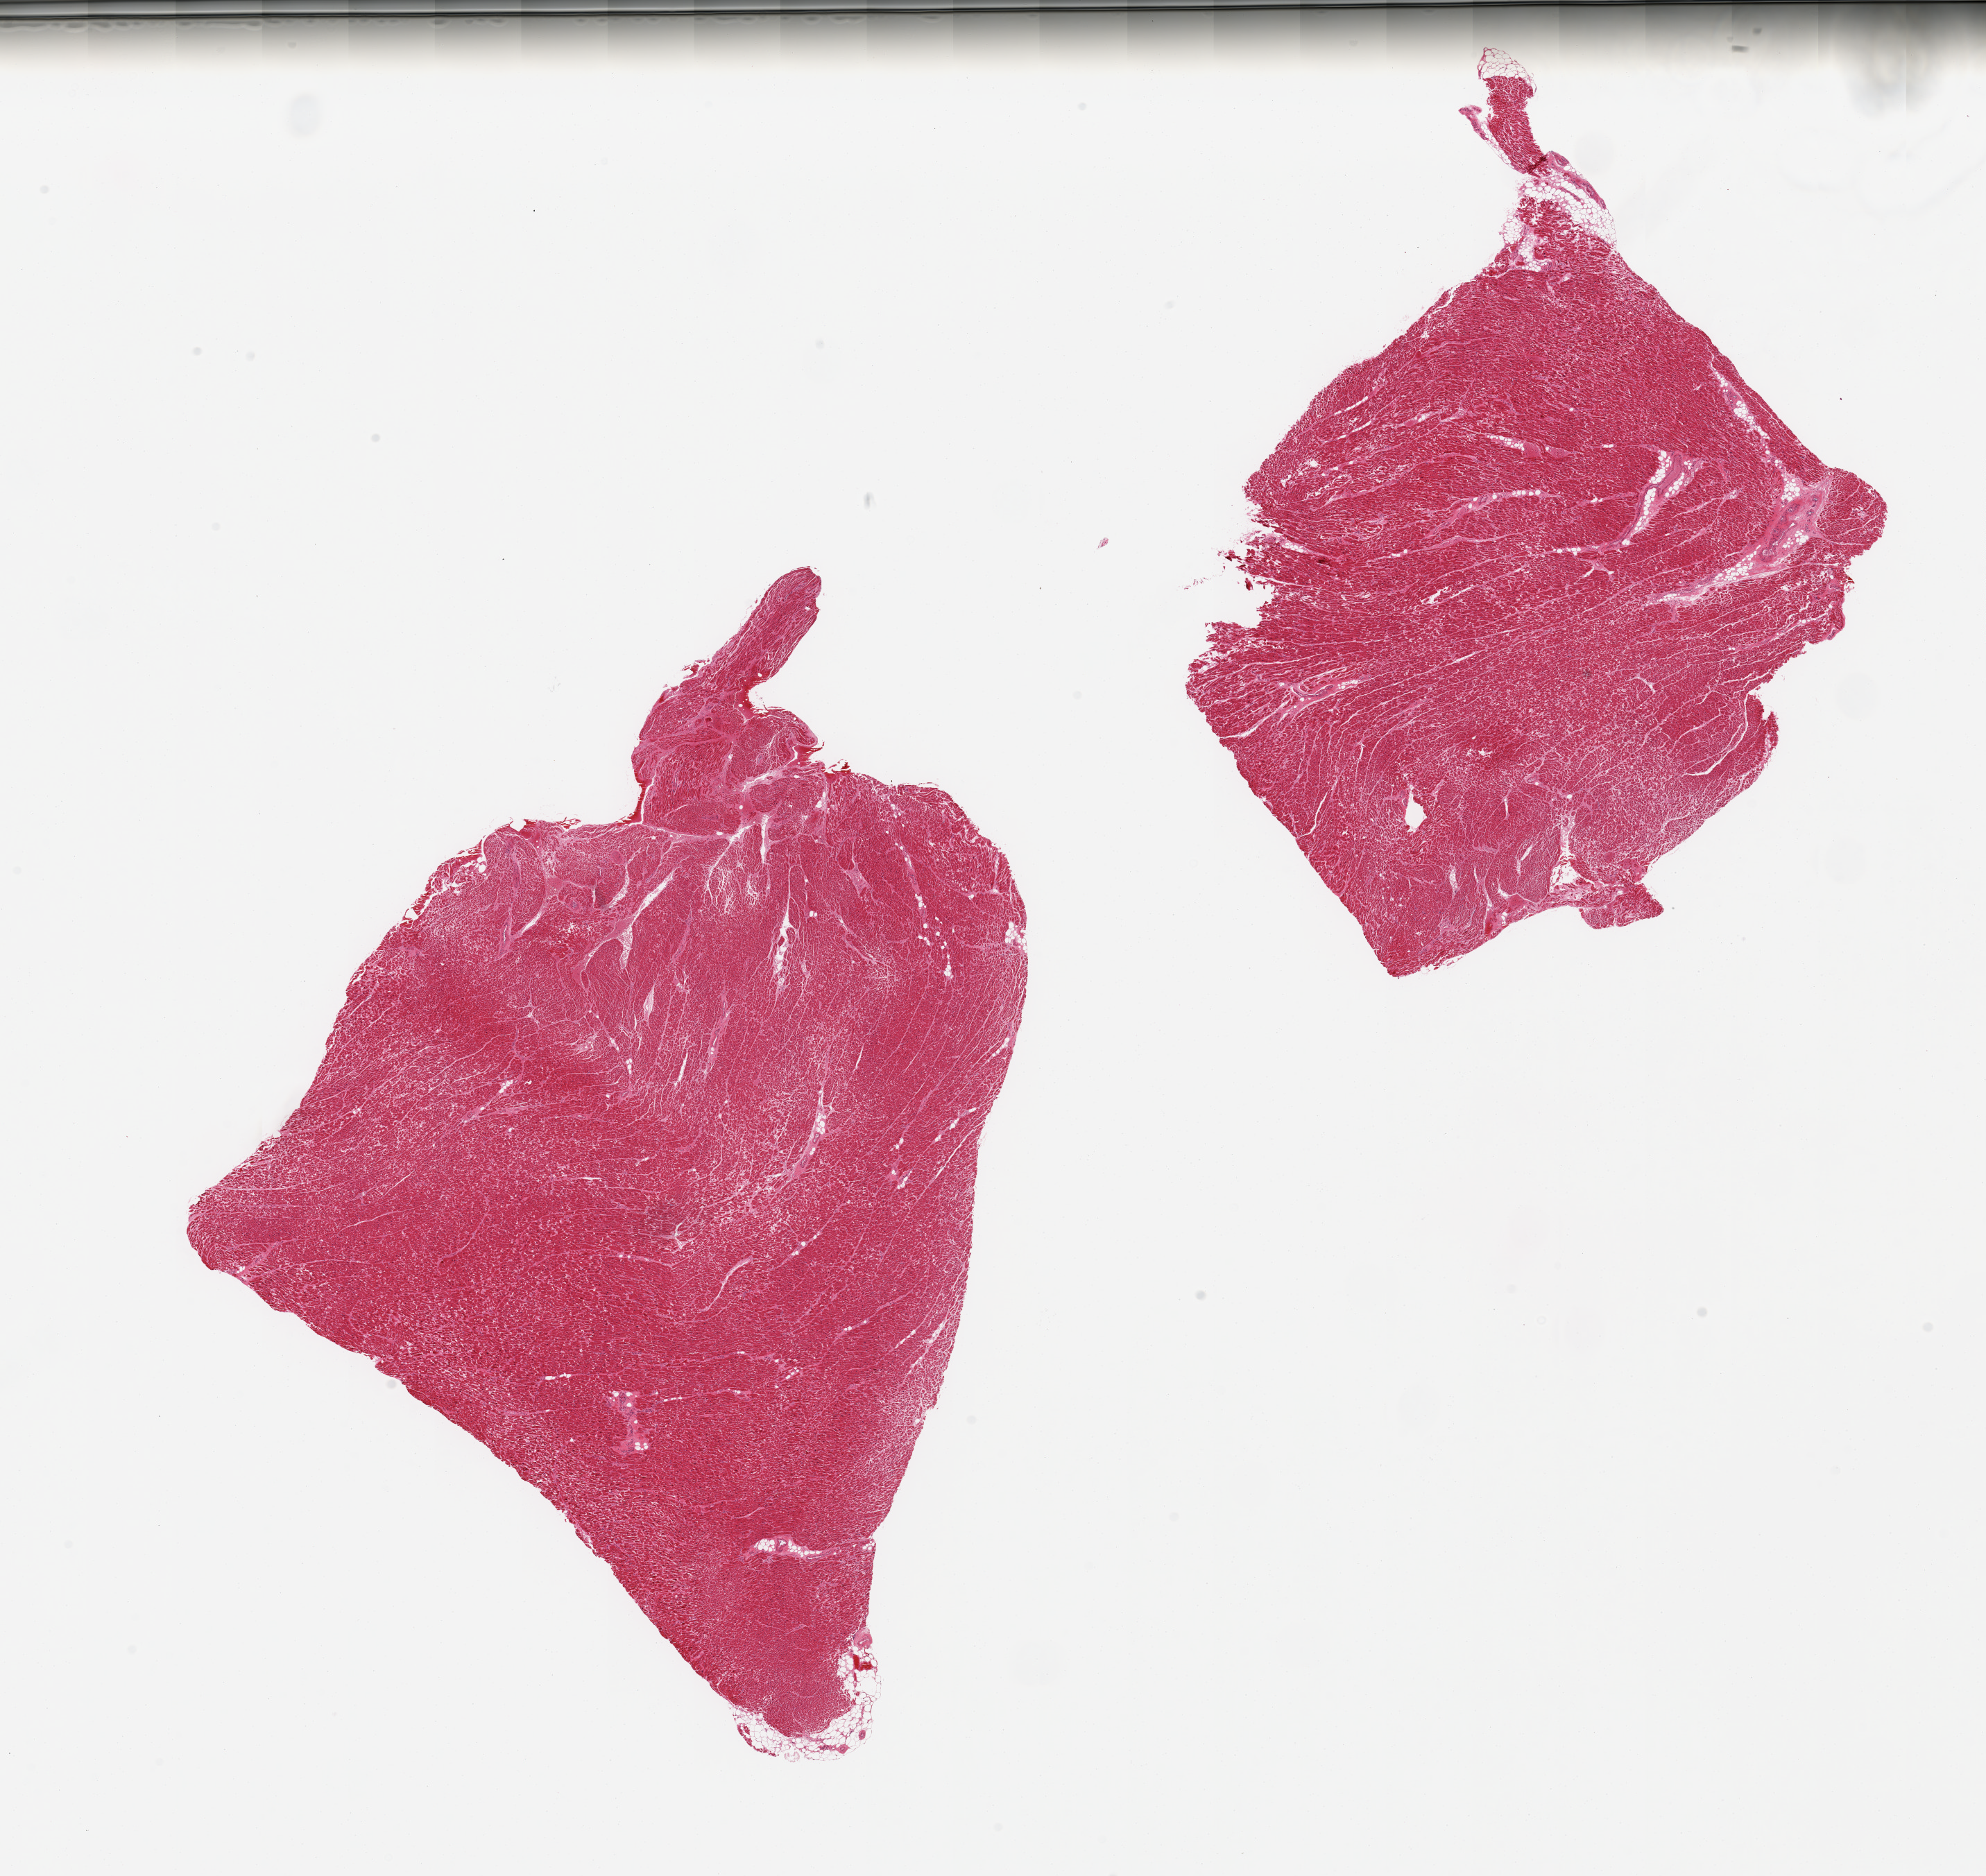
Digitized haematoxylin and eosin-stained section, whole scanned area (about 22.6 x 21.4 mm) shown as a low-resolution overview, PAXgene-fixed, paraffin-embedded tissue, target tissue: heart, tissue donor sample. Donor sex: male.
Review note (as recorded): 2 pieces; mild interstitial fibrosis.